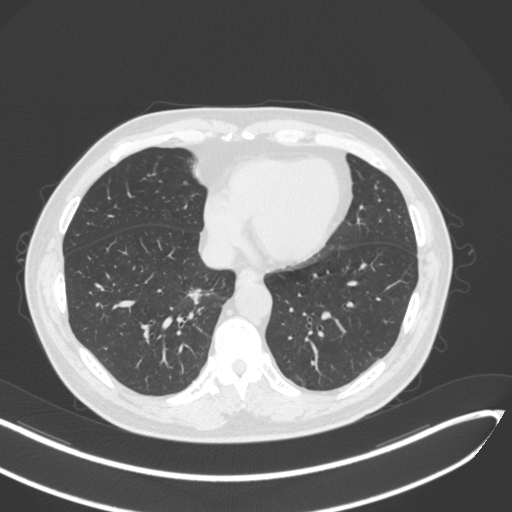
Chest CT, one axial slice; slice 121 of 429 in the series (ordered by position); 120 kVp; lung window (W 1500 / L -600 HU); 1 mm slice thickness; 512 × 512 image matrix, field of view 400 × 400 mm. Male patient, age 62 years. From the clinical record (not read from this slice): clinical TNM (as recorded): T1b N0 M0.
Annotated regions visible in this slice (rectangle marked by the reading radiologist):
- lung tumour (recorded histology: adenocarcinoma): bounding box (x1, y1, x2, y2) in pixels: (183, 283, 212, 306)